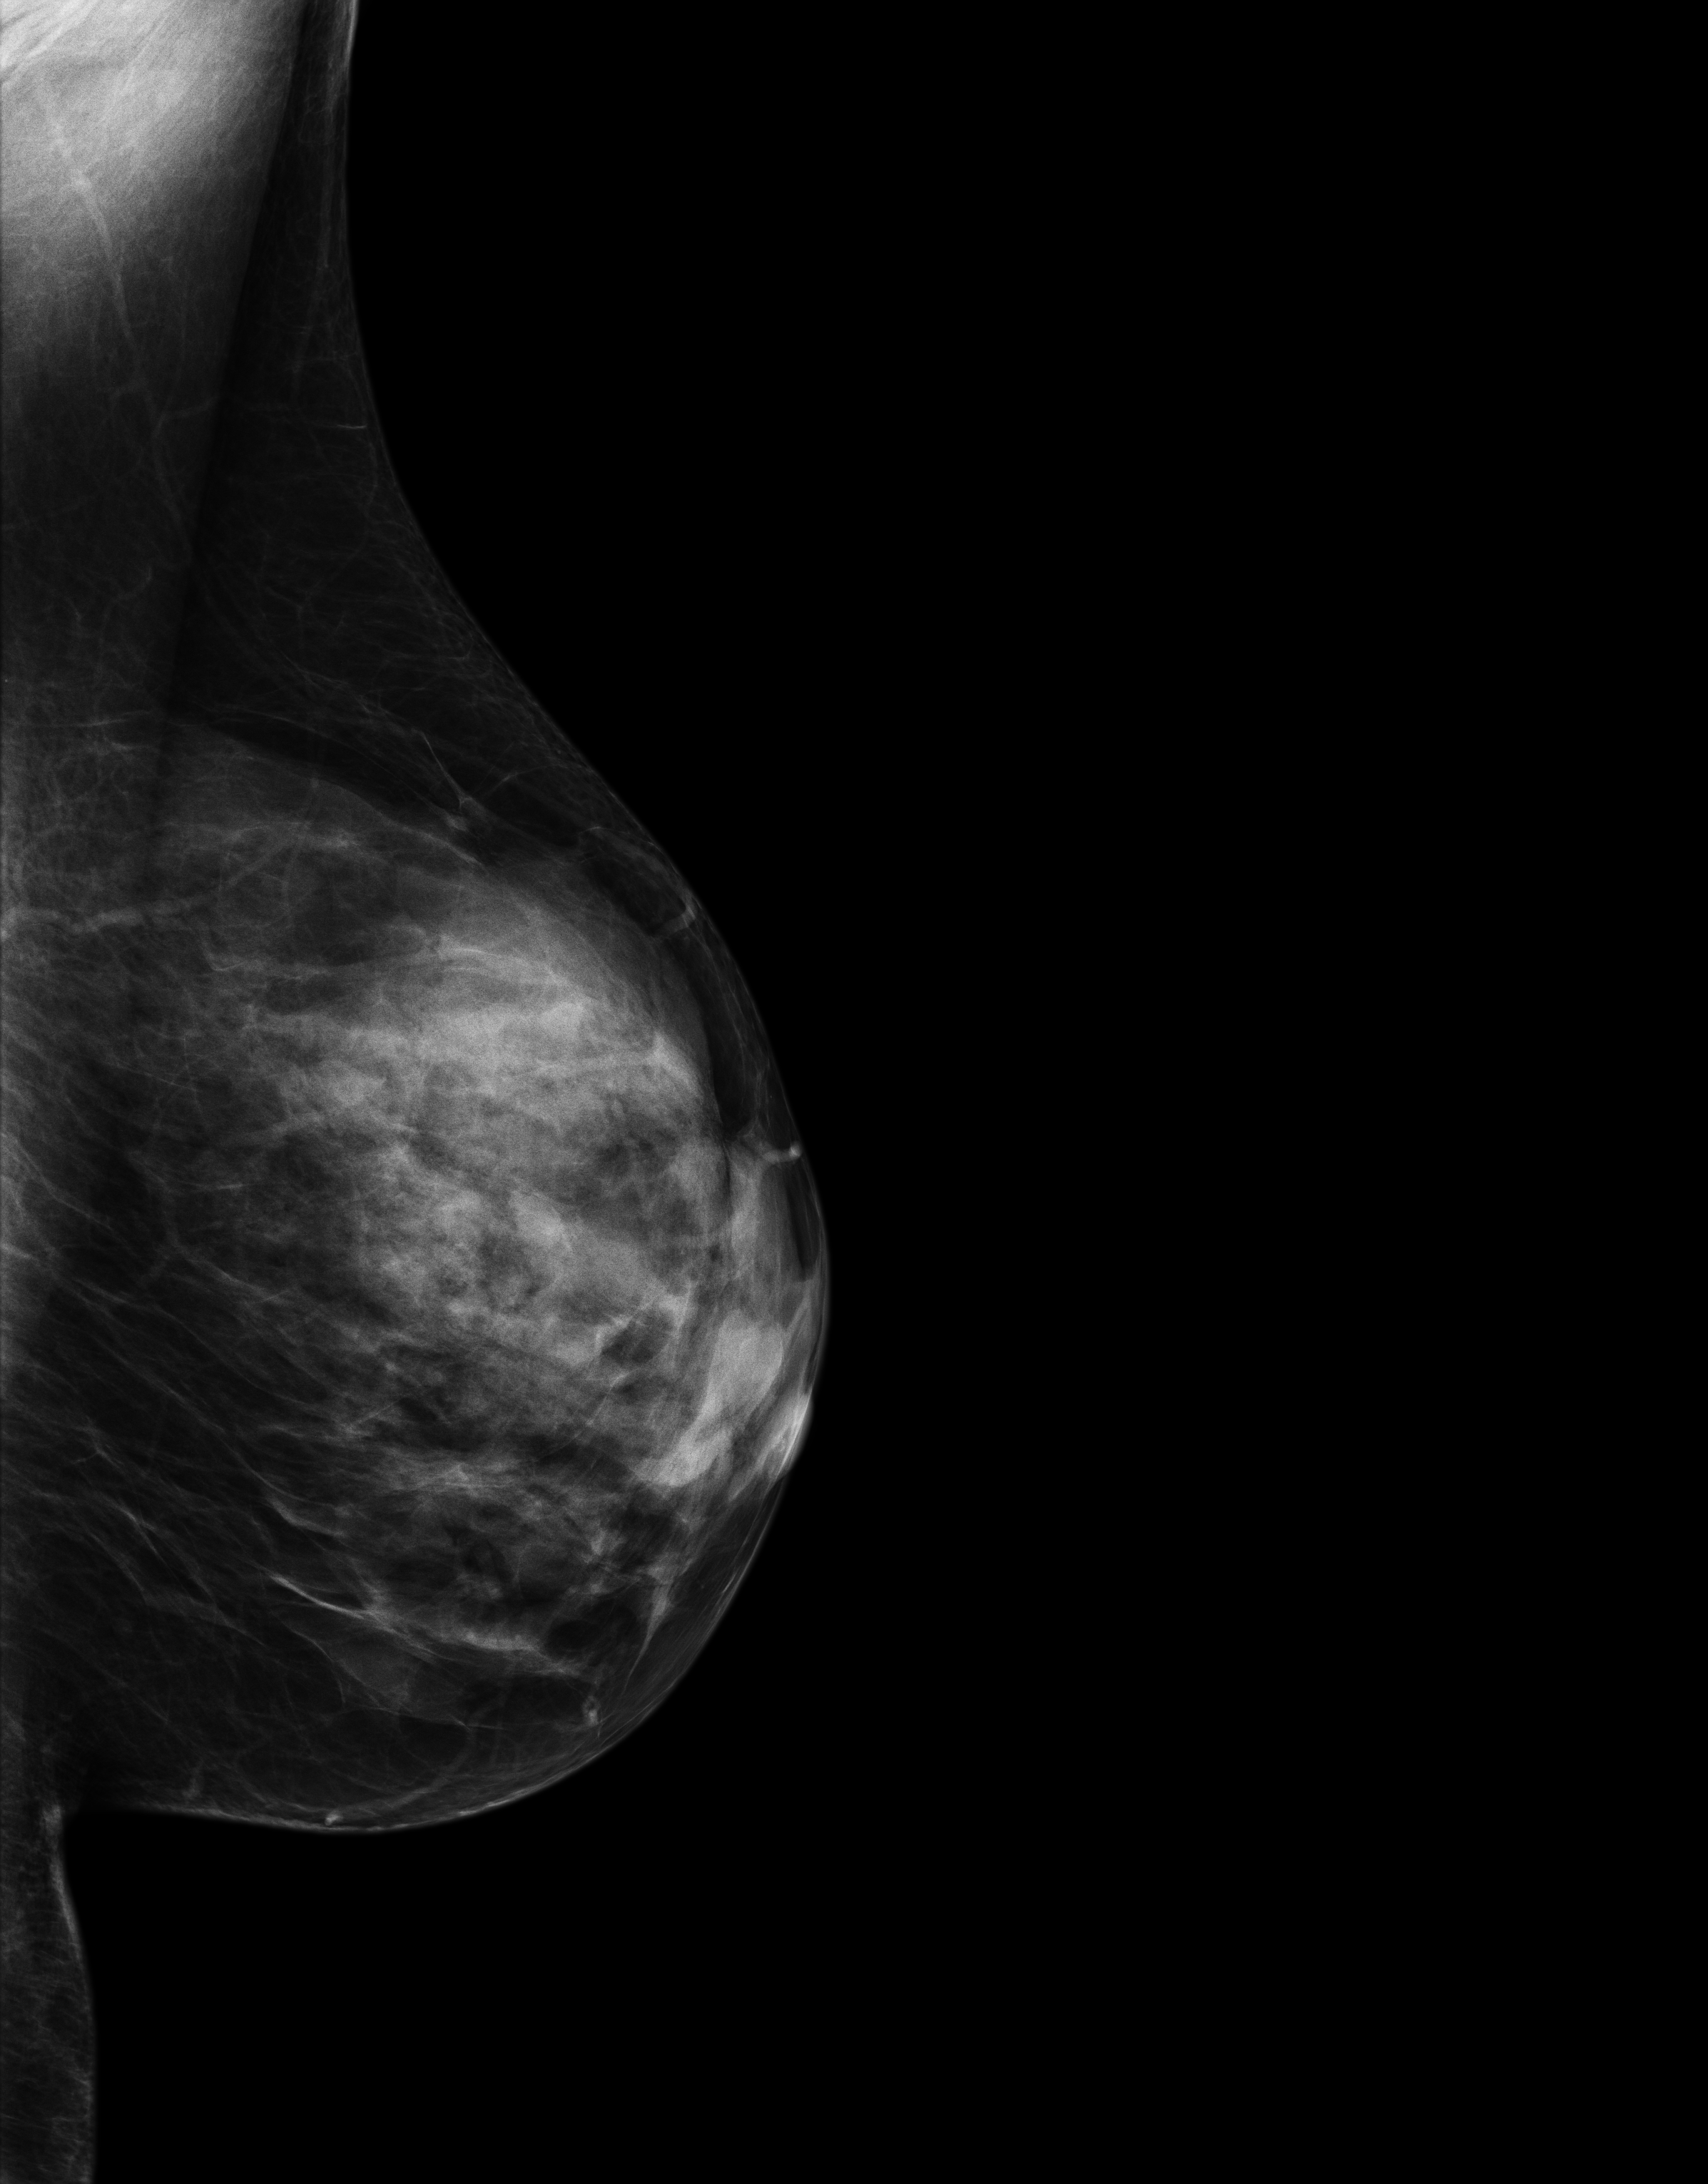
Screening examination, system: Senographe Essential ADS_56.21.3. Patient aged 61 years (female).
Image type: full-field digital mammogram. Breast: left. Projection: MLO view.